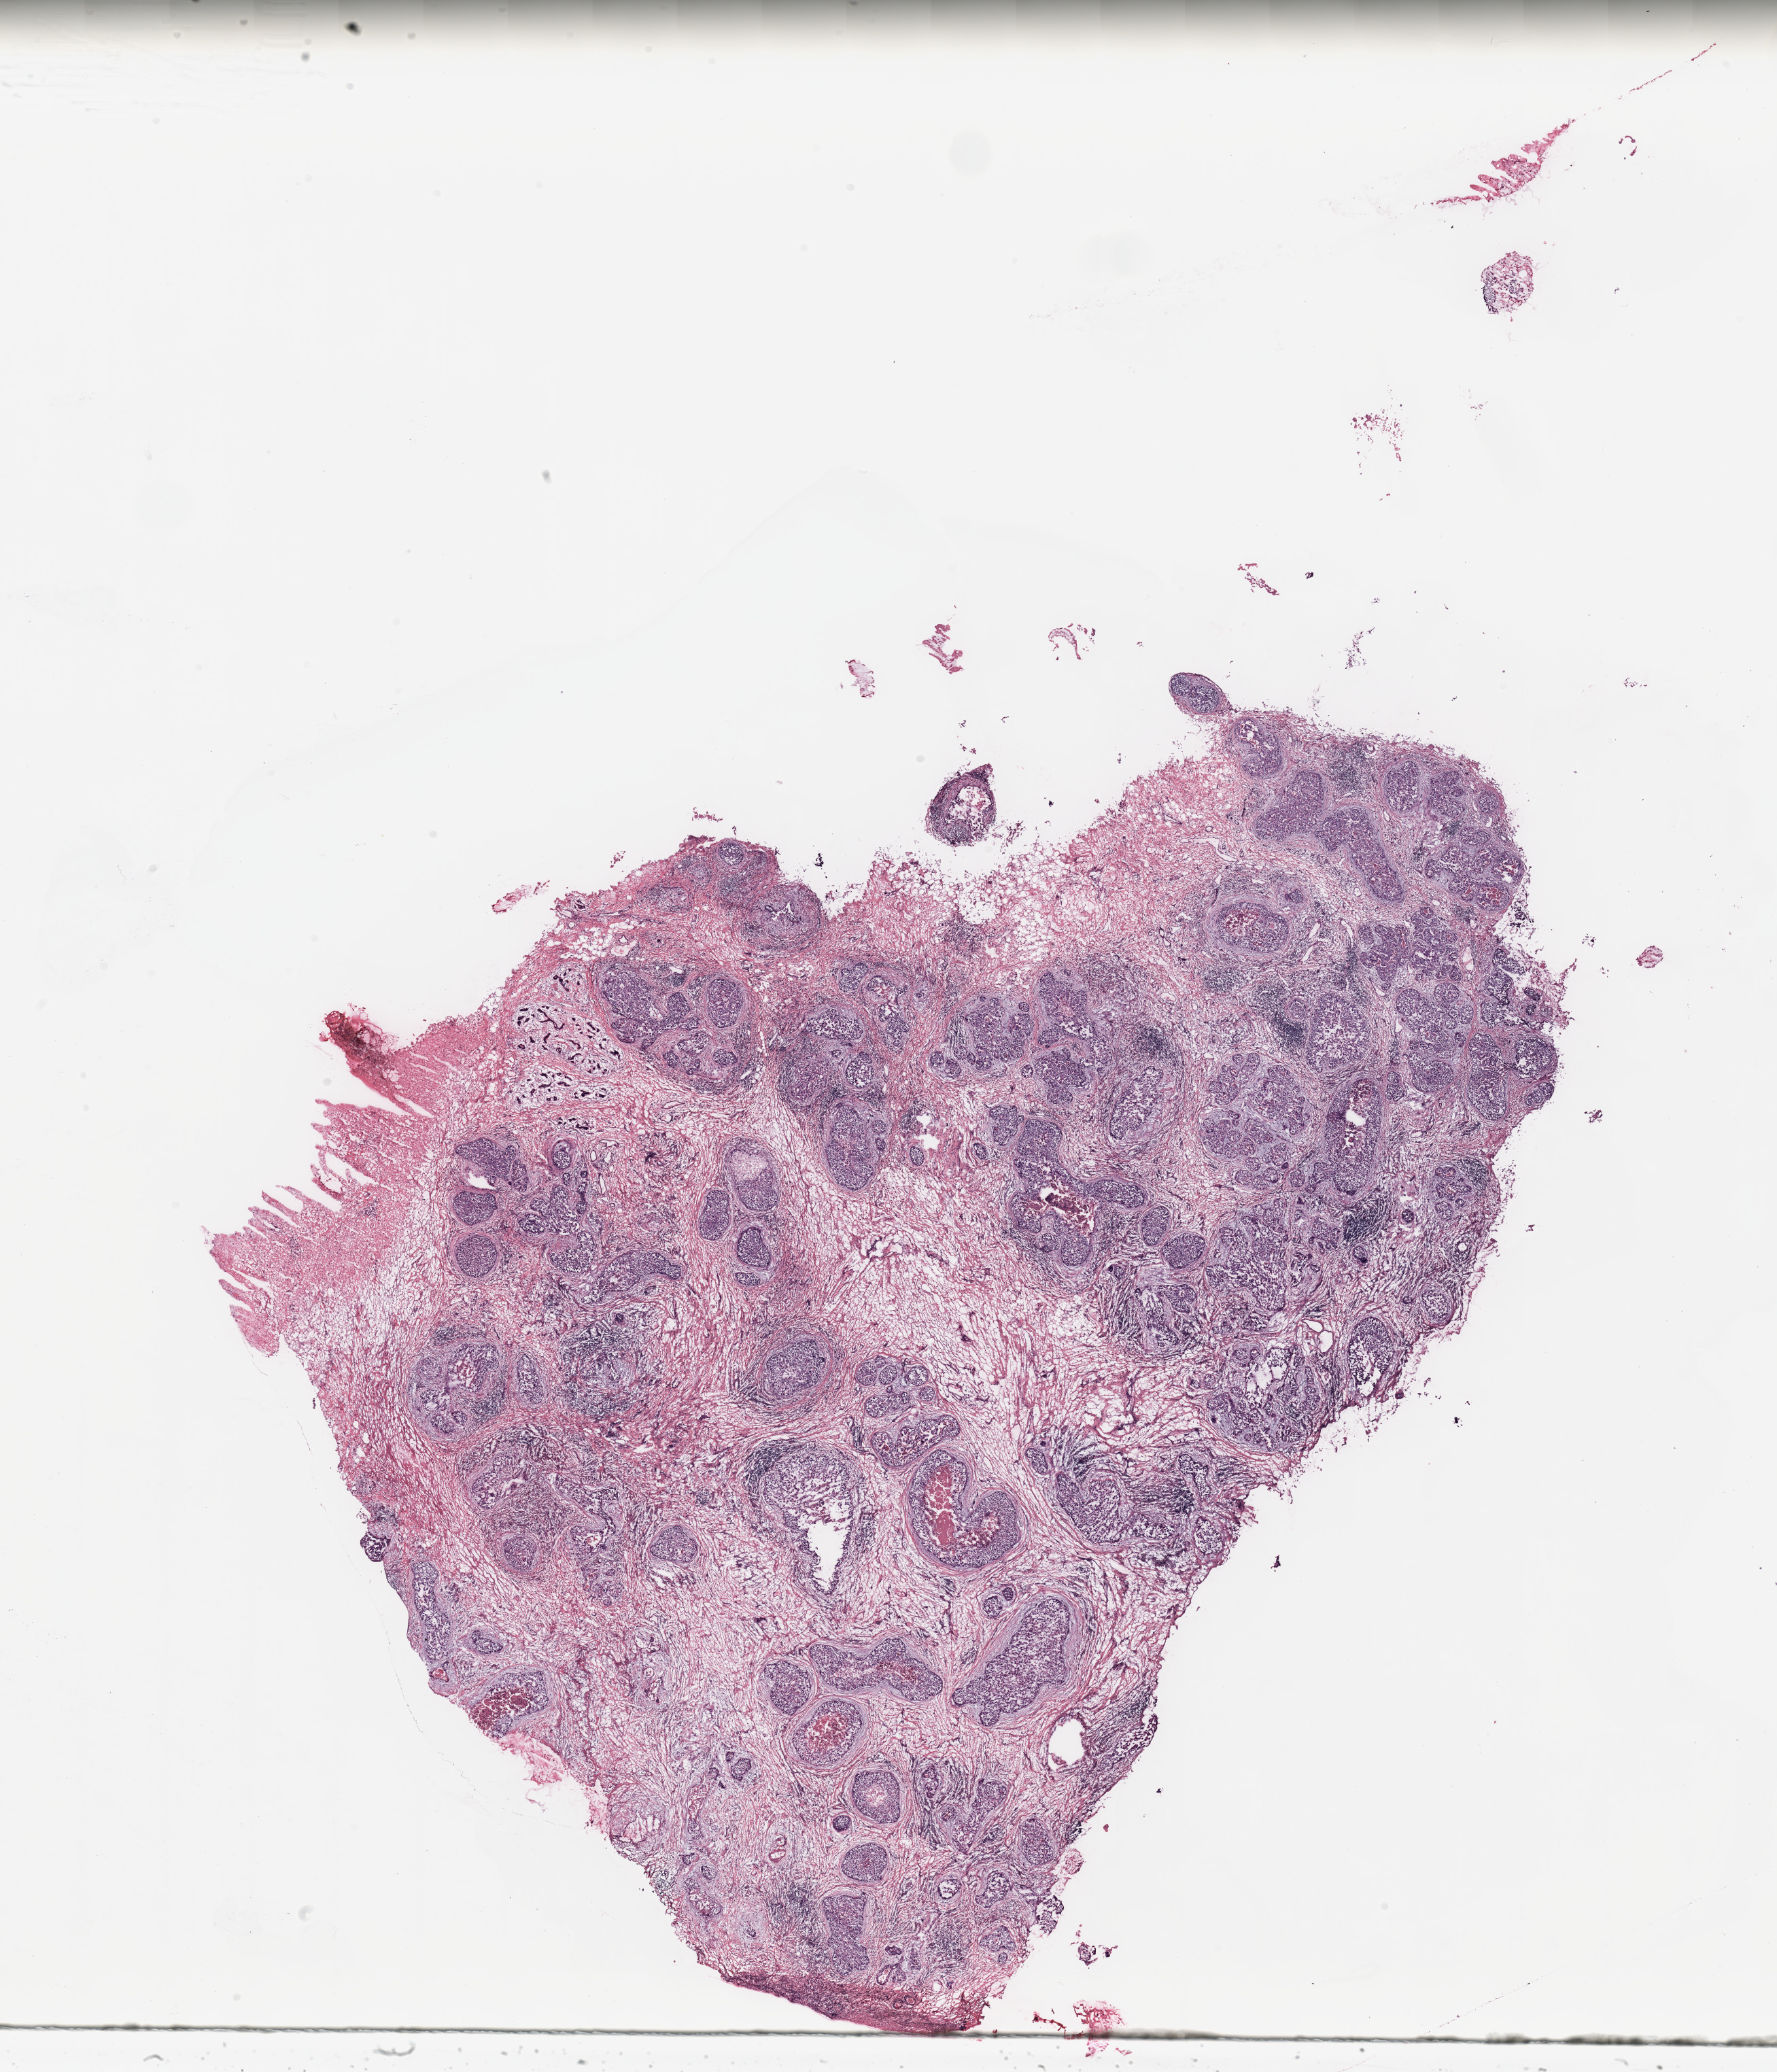
Digitized H&E-stained tissue section (whole slide) — shown as a low-resolution overview of the whole scanned area (about 20.7 x 24.1 mm, slide scanned at 20x), breast, tissue type not recorded.
Patient diagnosis (cohort enrolment): breast cancer (breast).